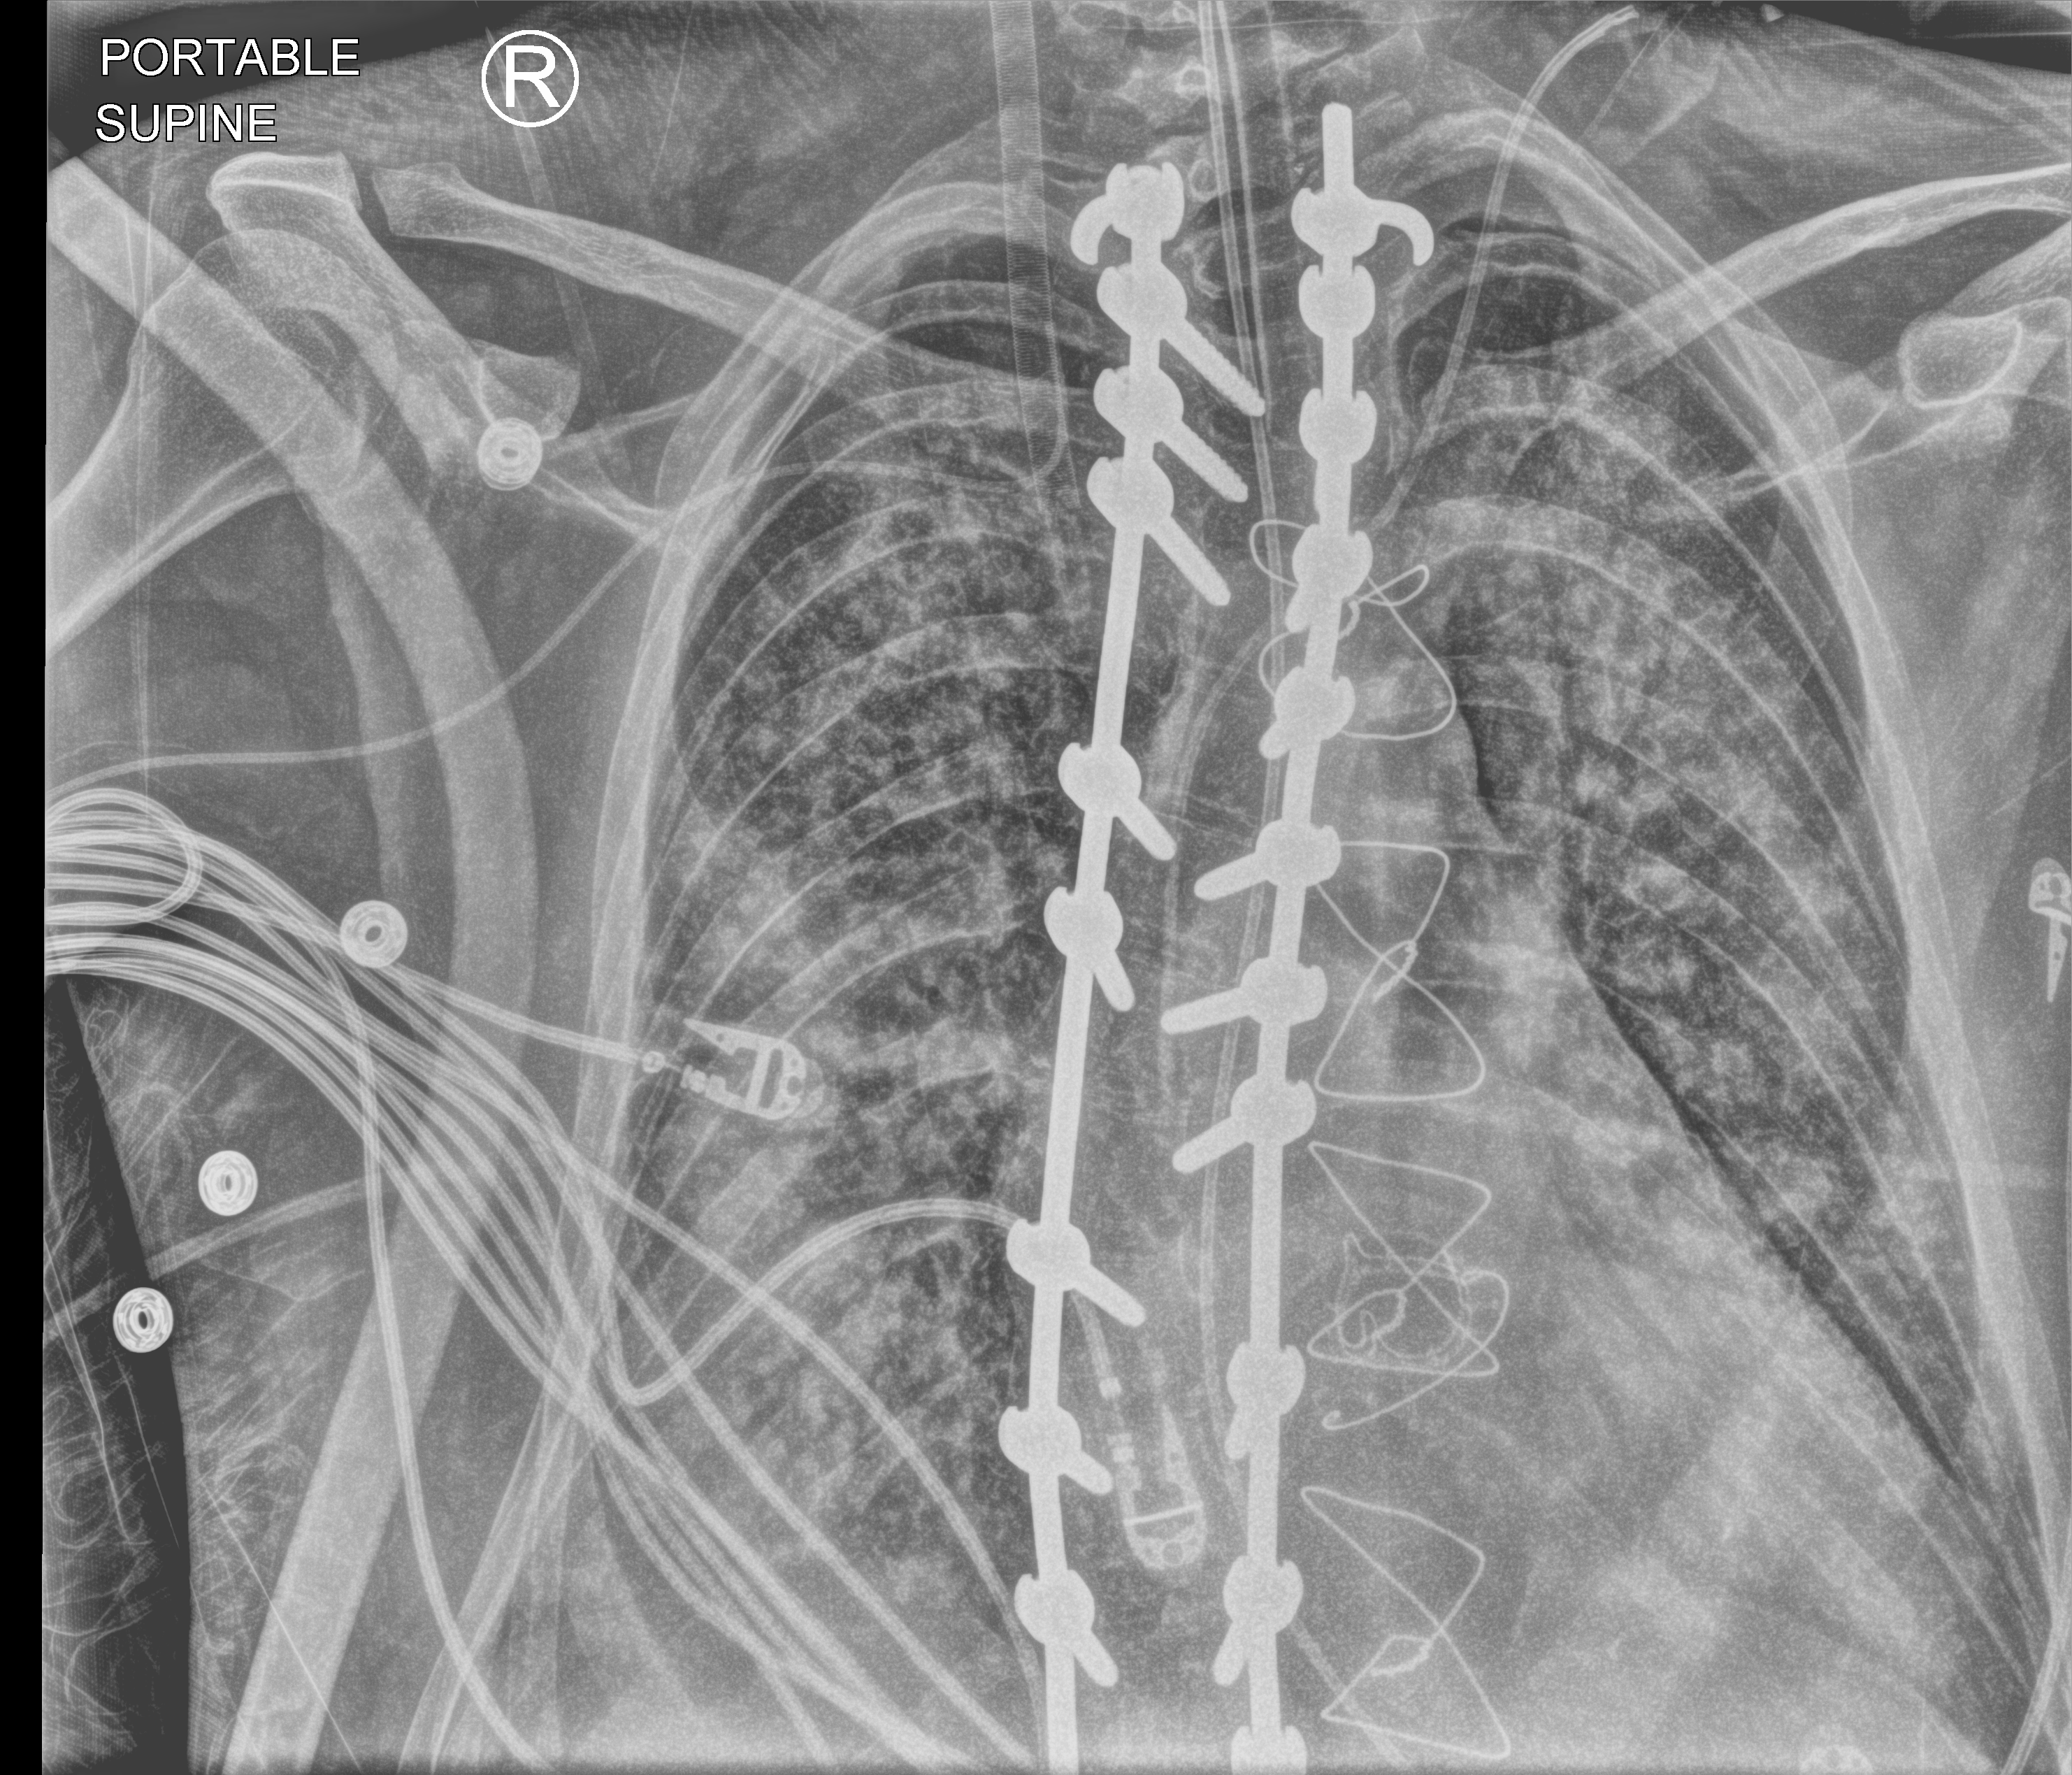
Portable chest radiograph, anteroposterior (AP) projection. Adult patient hospitalised with COVID-19, age 18–59 years.
Hospital-stay facts (about this admission, not read from this image; timing relative to this image not recorded): mechanically ventilated during this hospital stay: yes.